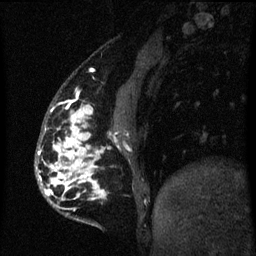
Breast MRI (dynamic contrast-enhanced), one sagittal slice; slice 17 of 60 in the series (ordered by position); dynamic contrast-enhanced series, image 2 of 3 at this slice position (ordered by acquisition); 1.5 T; TE 4.2 ms, TR 8 ms; 2 mm slice thickness; 256 × 256 image matrix, field of view 190 × 190 mm. Female patient, age 50 years.
Outlined on this slice (semi-automatic segmentation, software-assisted and operator-edited):
- analysis volume of interest (the breast-tissue region the enhancement analysis was run in; not a lesion): bounding box (x1, y1, x2, y2) in pixels: (35, 106, 104, 203)
- tumour enhancement mask (voxels above the 70 % enhancement threshold inside the analysis volume of interest): (36, 107, 102, 197)